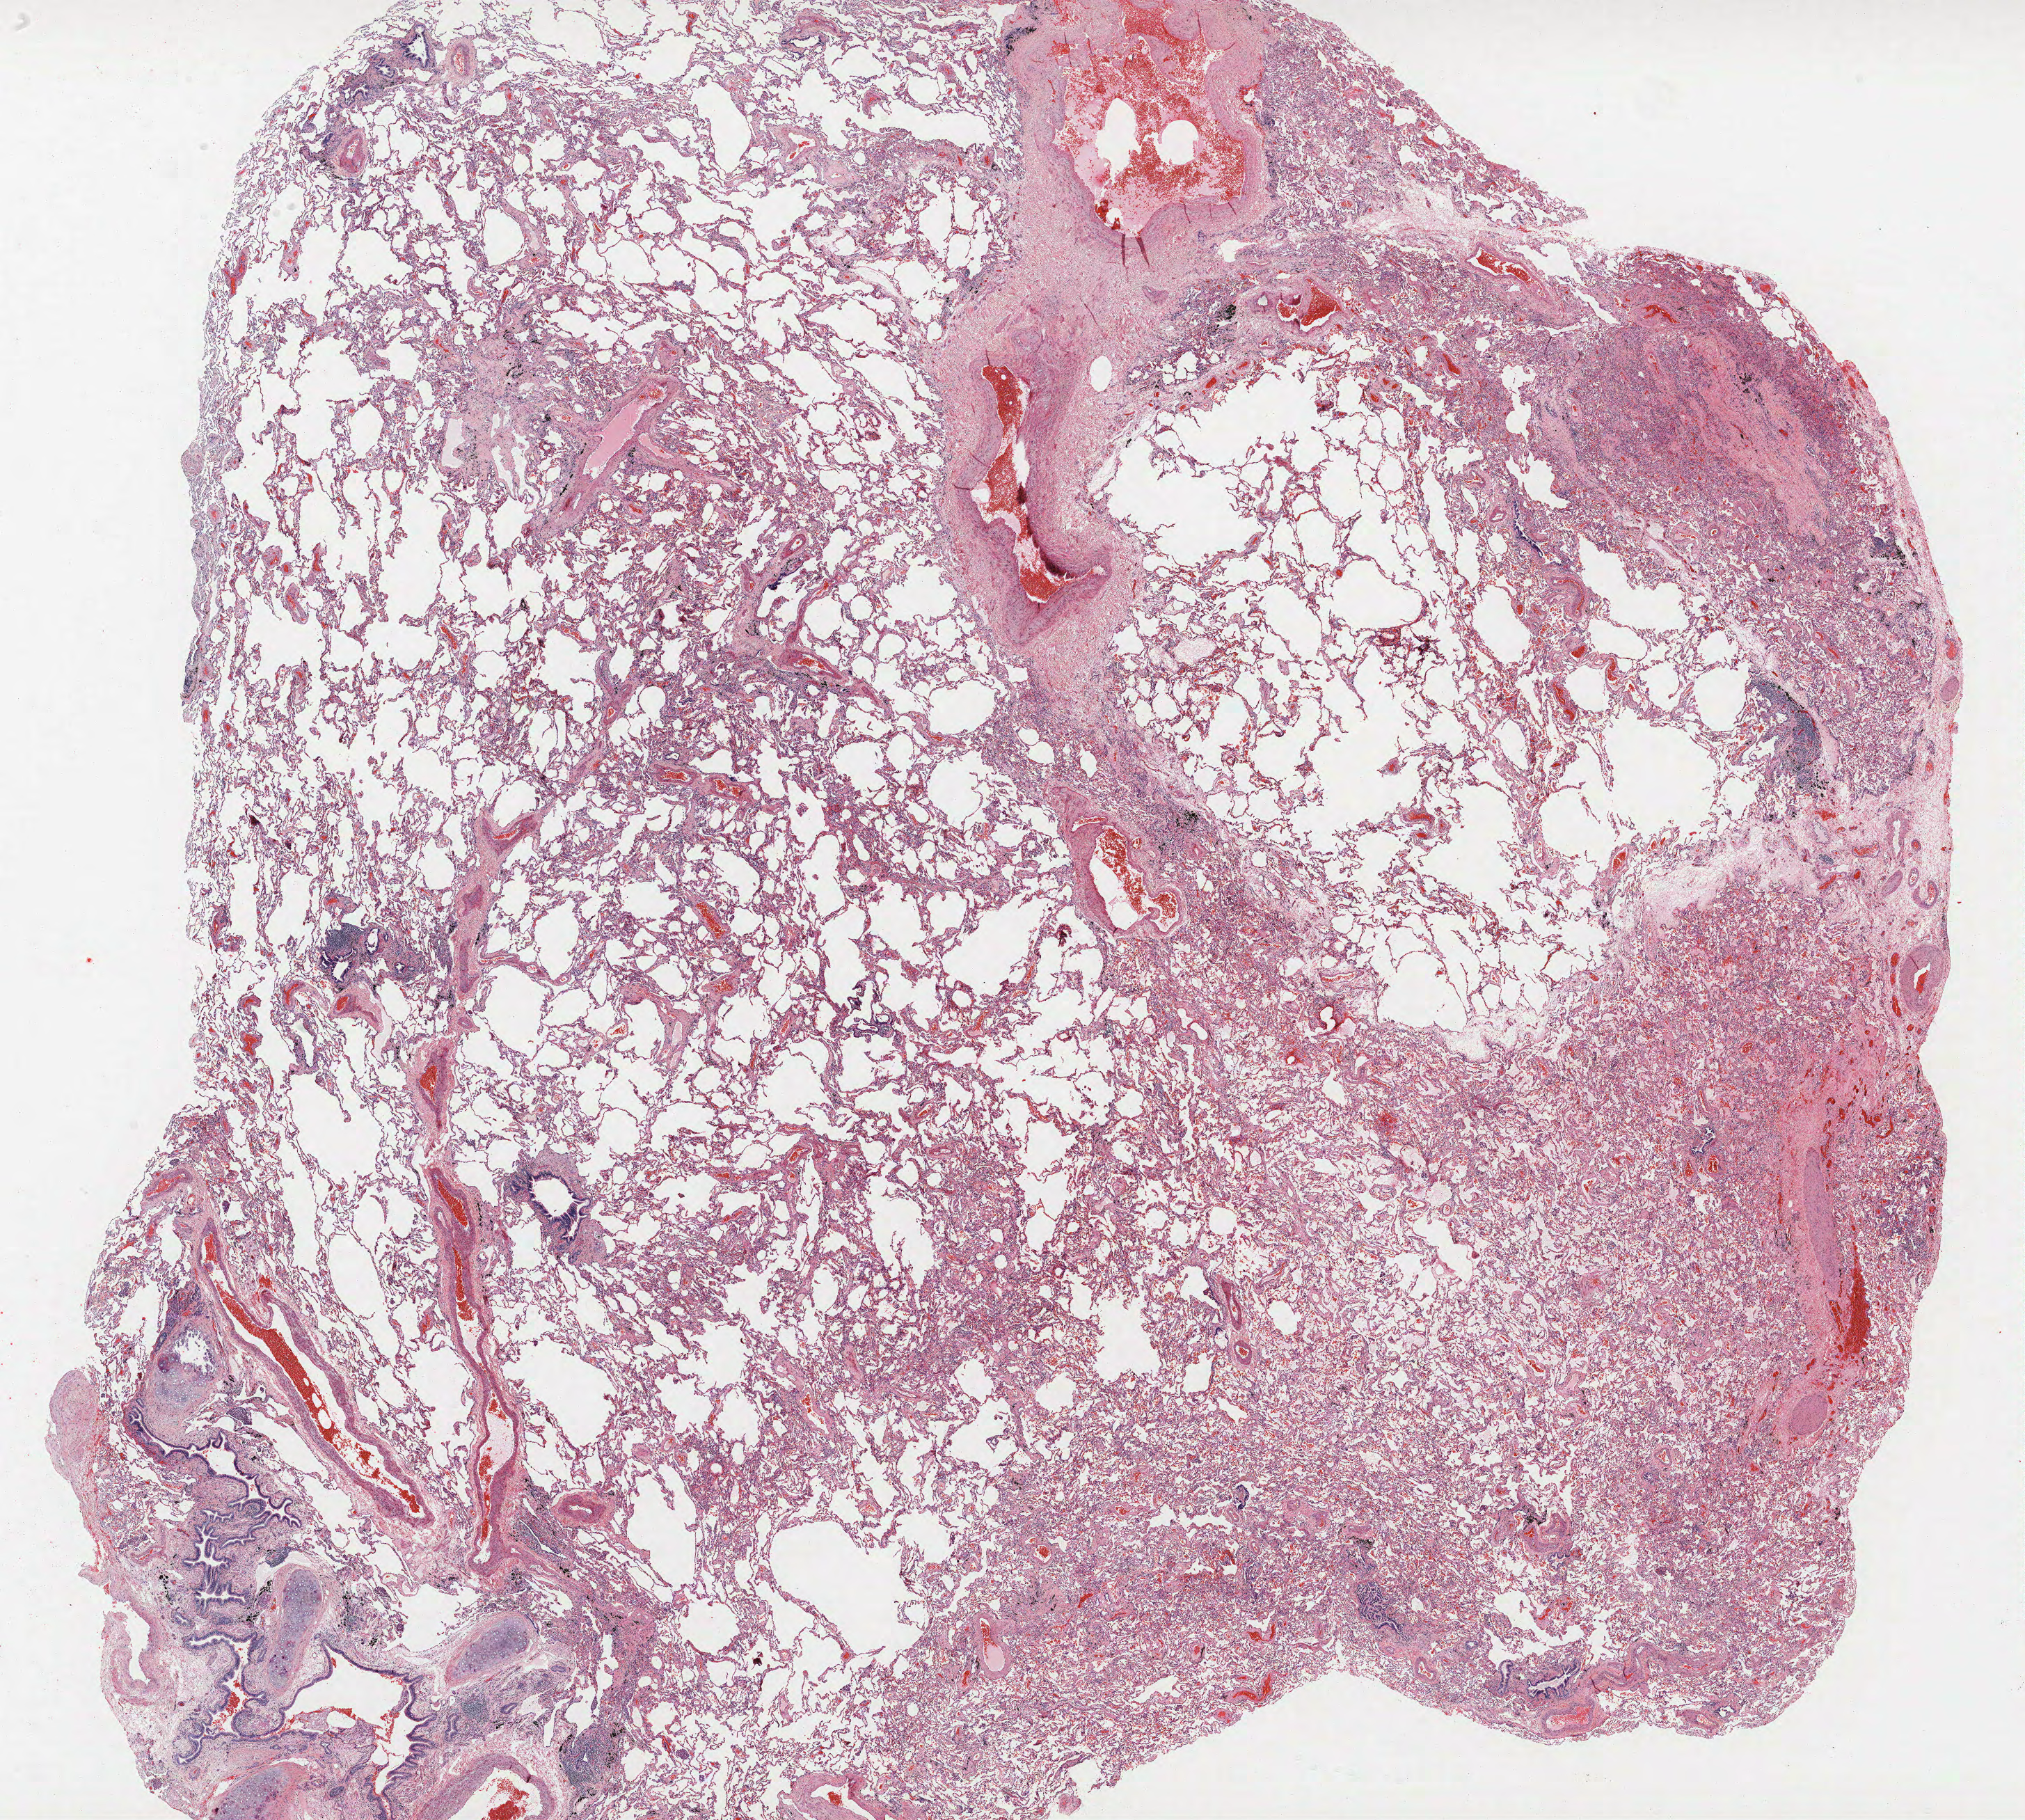
Whole-slide histology image, H&E, a low-resolution overview of the entire scanned area, about 23.3 x 20.9 mm (from a 40x scan); FFPE section; lung. Male, age 72 at enrolment. Grade: moderately differentiated (G2).
Tumour size (pathology): 12 mm. Primary tumour location (clinical record): right upper lobe. Participant's lung-cancer diagnosis: Adenocarcinoma, NOS. Stage (AJCC 6th edition): IIA.